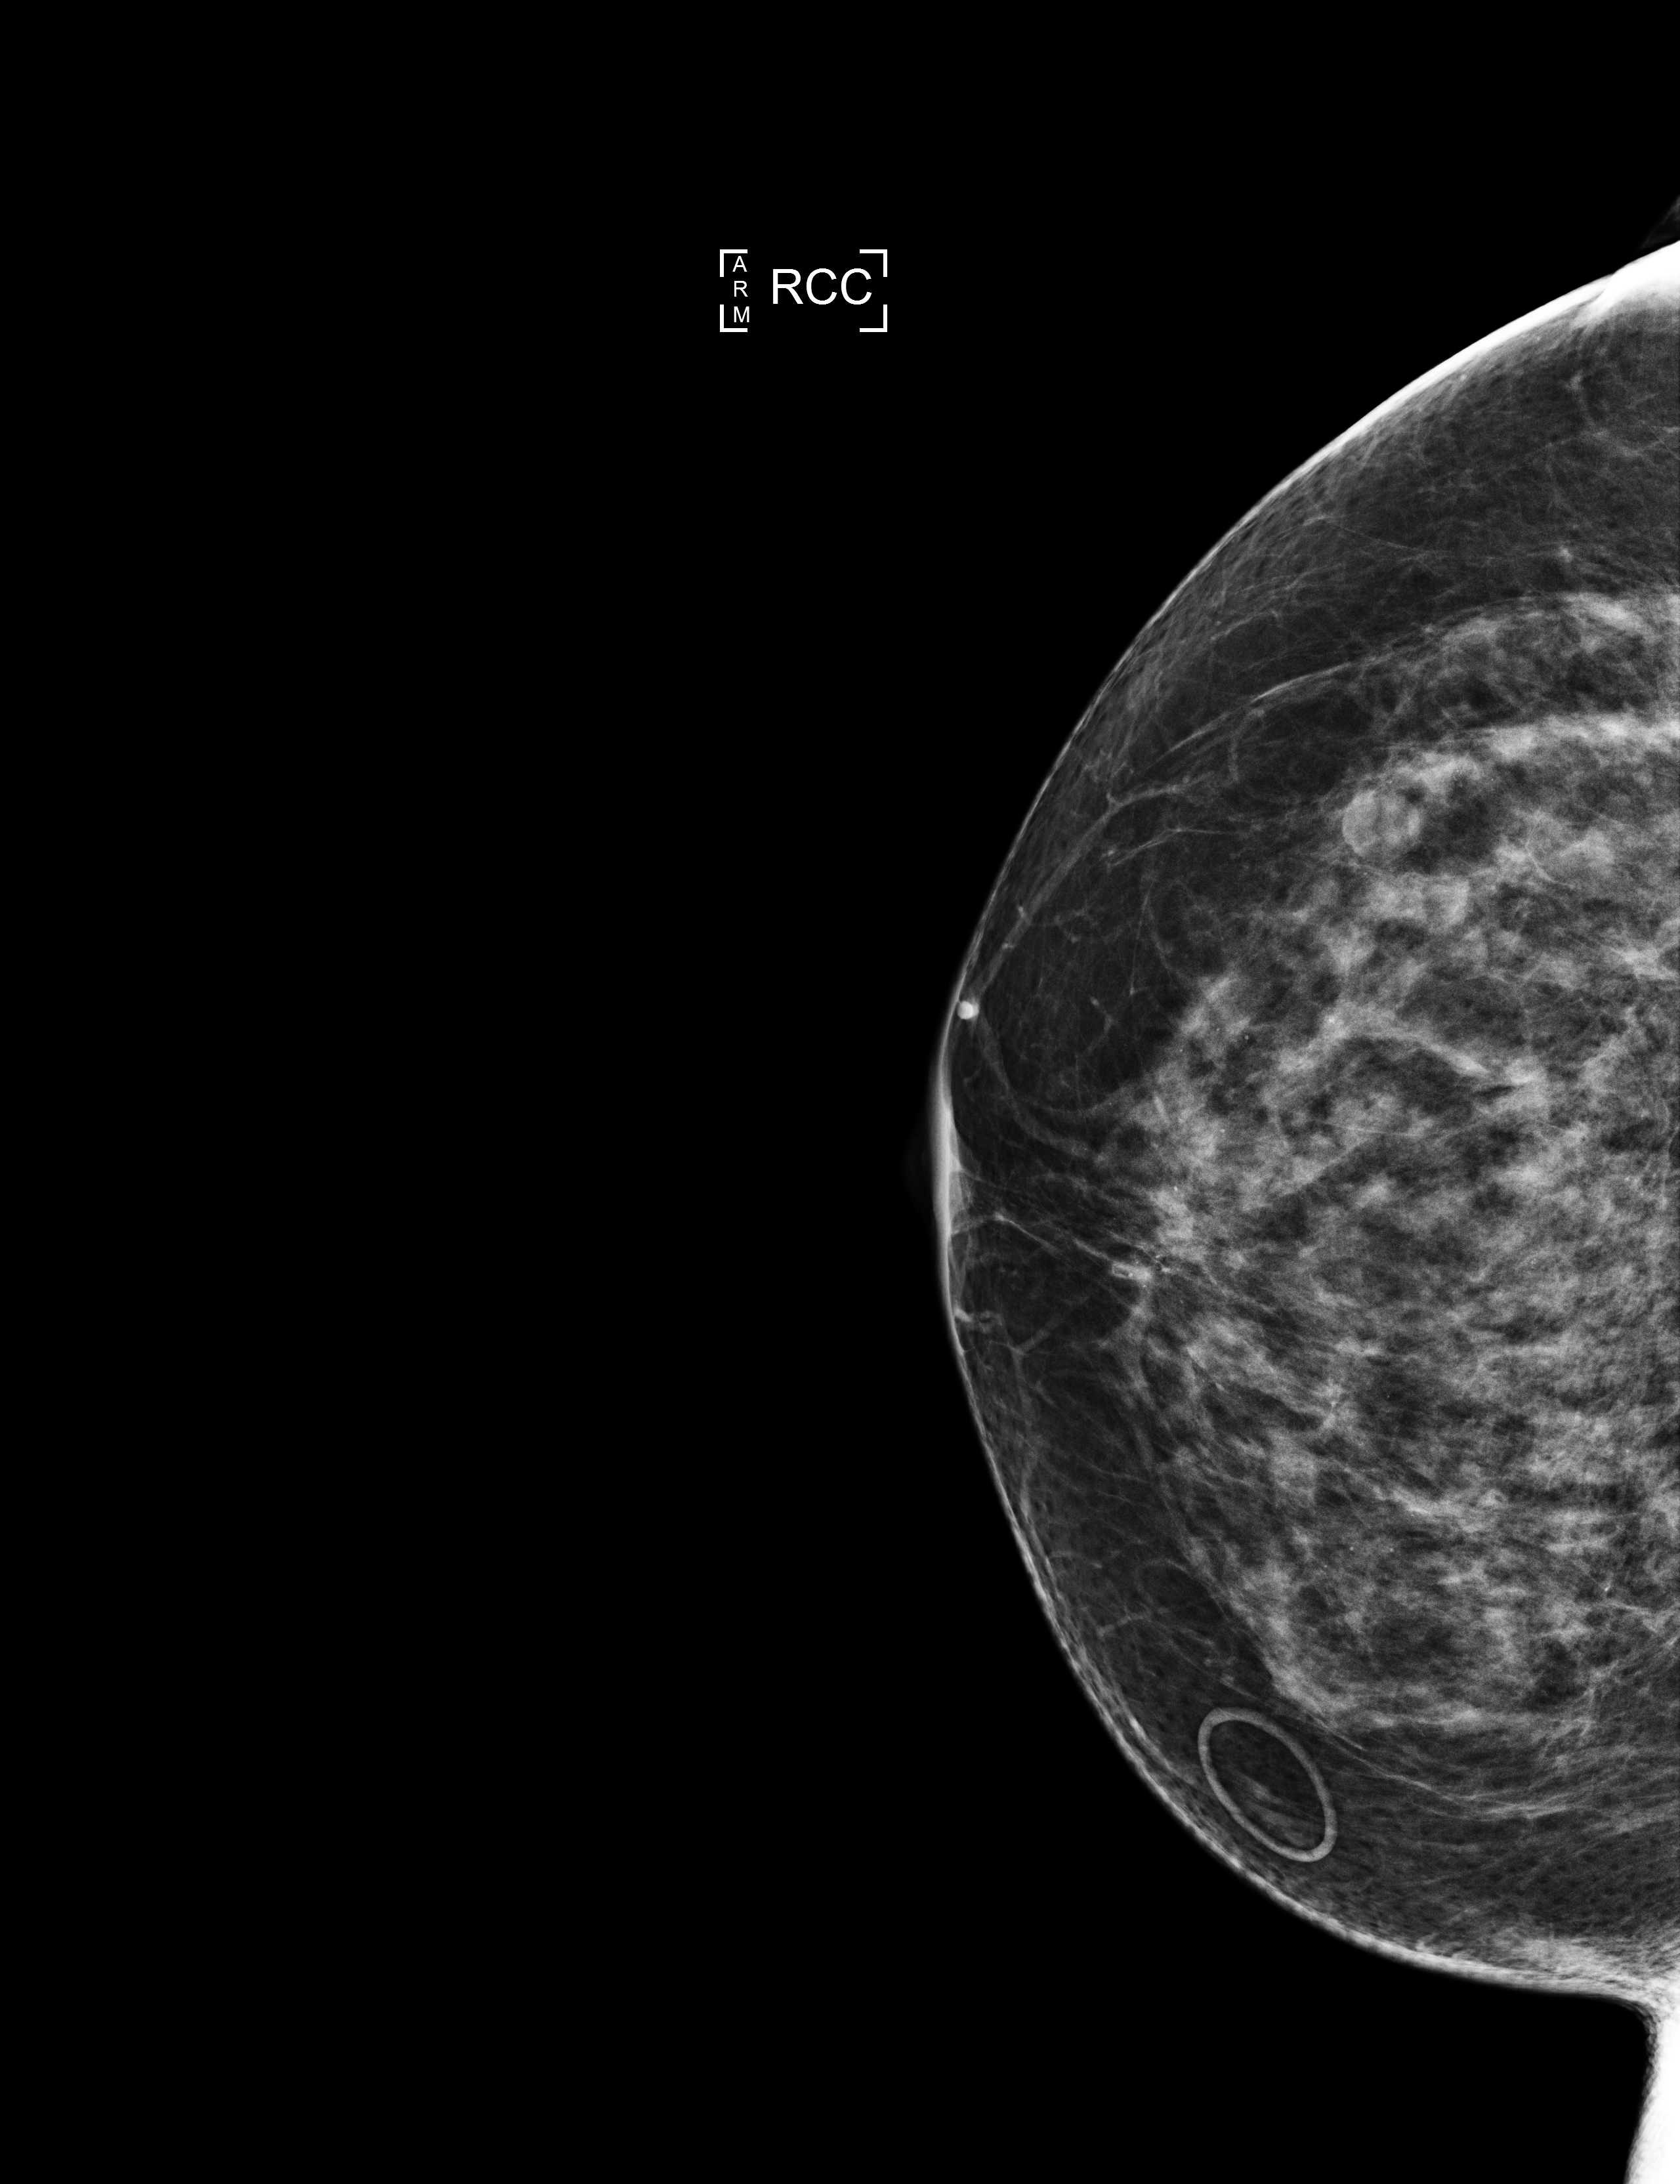
Annual screening mammography examination.
Image type: full-field digital mammogram. Breast: right. Projection: CC view.